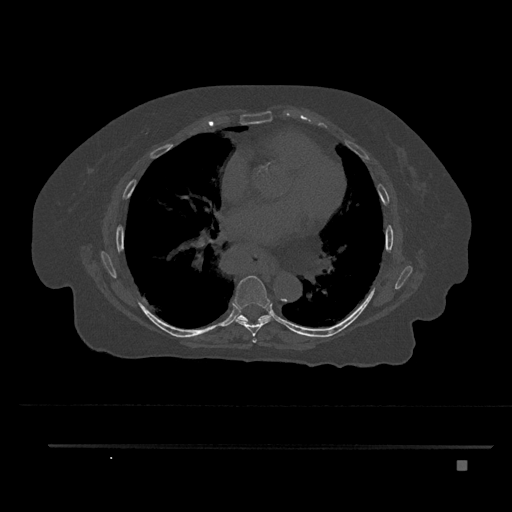
CT including the spine, one axial slice. Slice 472 of 797 in the series (ordered by position). Reconstruction kernel Br40s/3. 120 kVp. Bone window (W 1800 / L 400 HU). 0.5 mm slice thickness. 512 × 512 image matrix. Female patient, age 76 years. From the clinical record (not read from this slice): primary cancer: lung.
Structures marked on this image (semi-automatic segmentation, software-assisted and operator-edited):
- T6 vertebra: bounding box (x1, y1, x2, y2) in pixels: (252, 338, 257, 343)
- T7 vertebra: (234, 276, 273, 337)
- T8 vertebra: (236, 314, 270, 321)